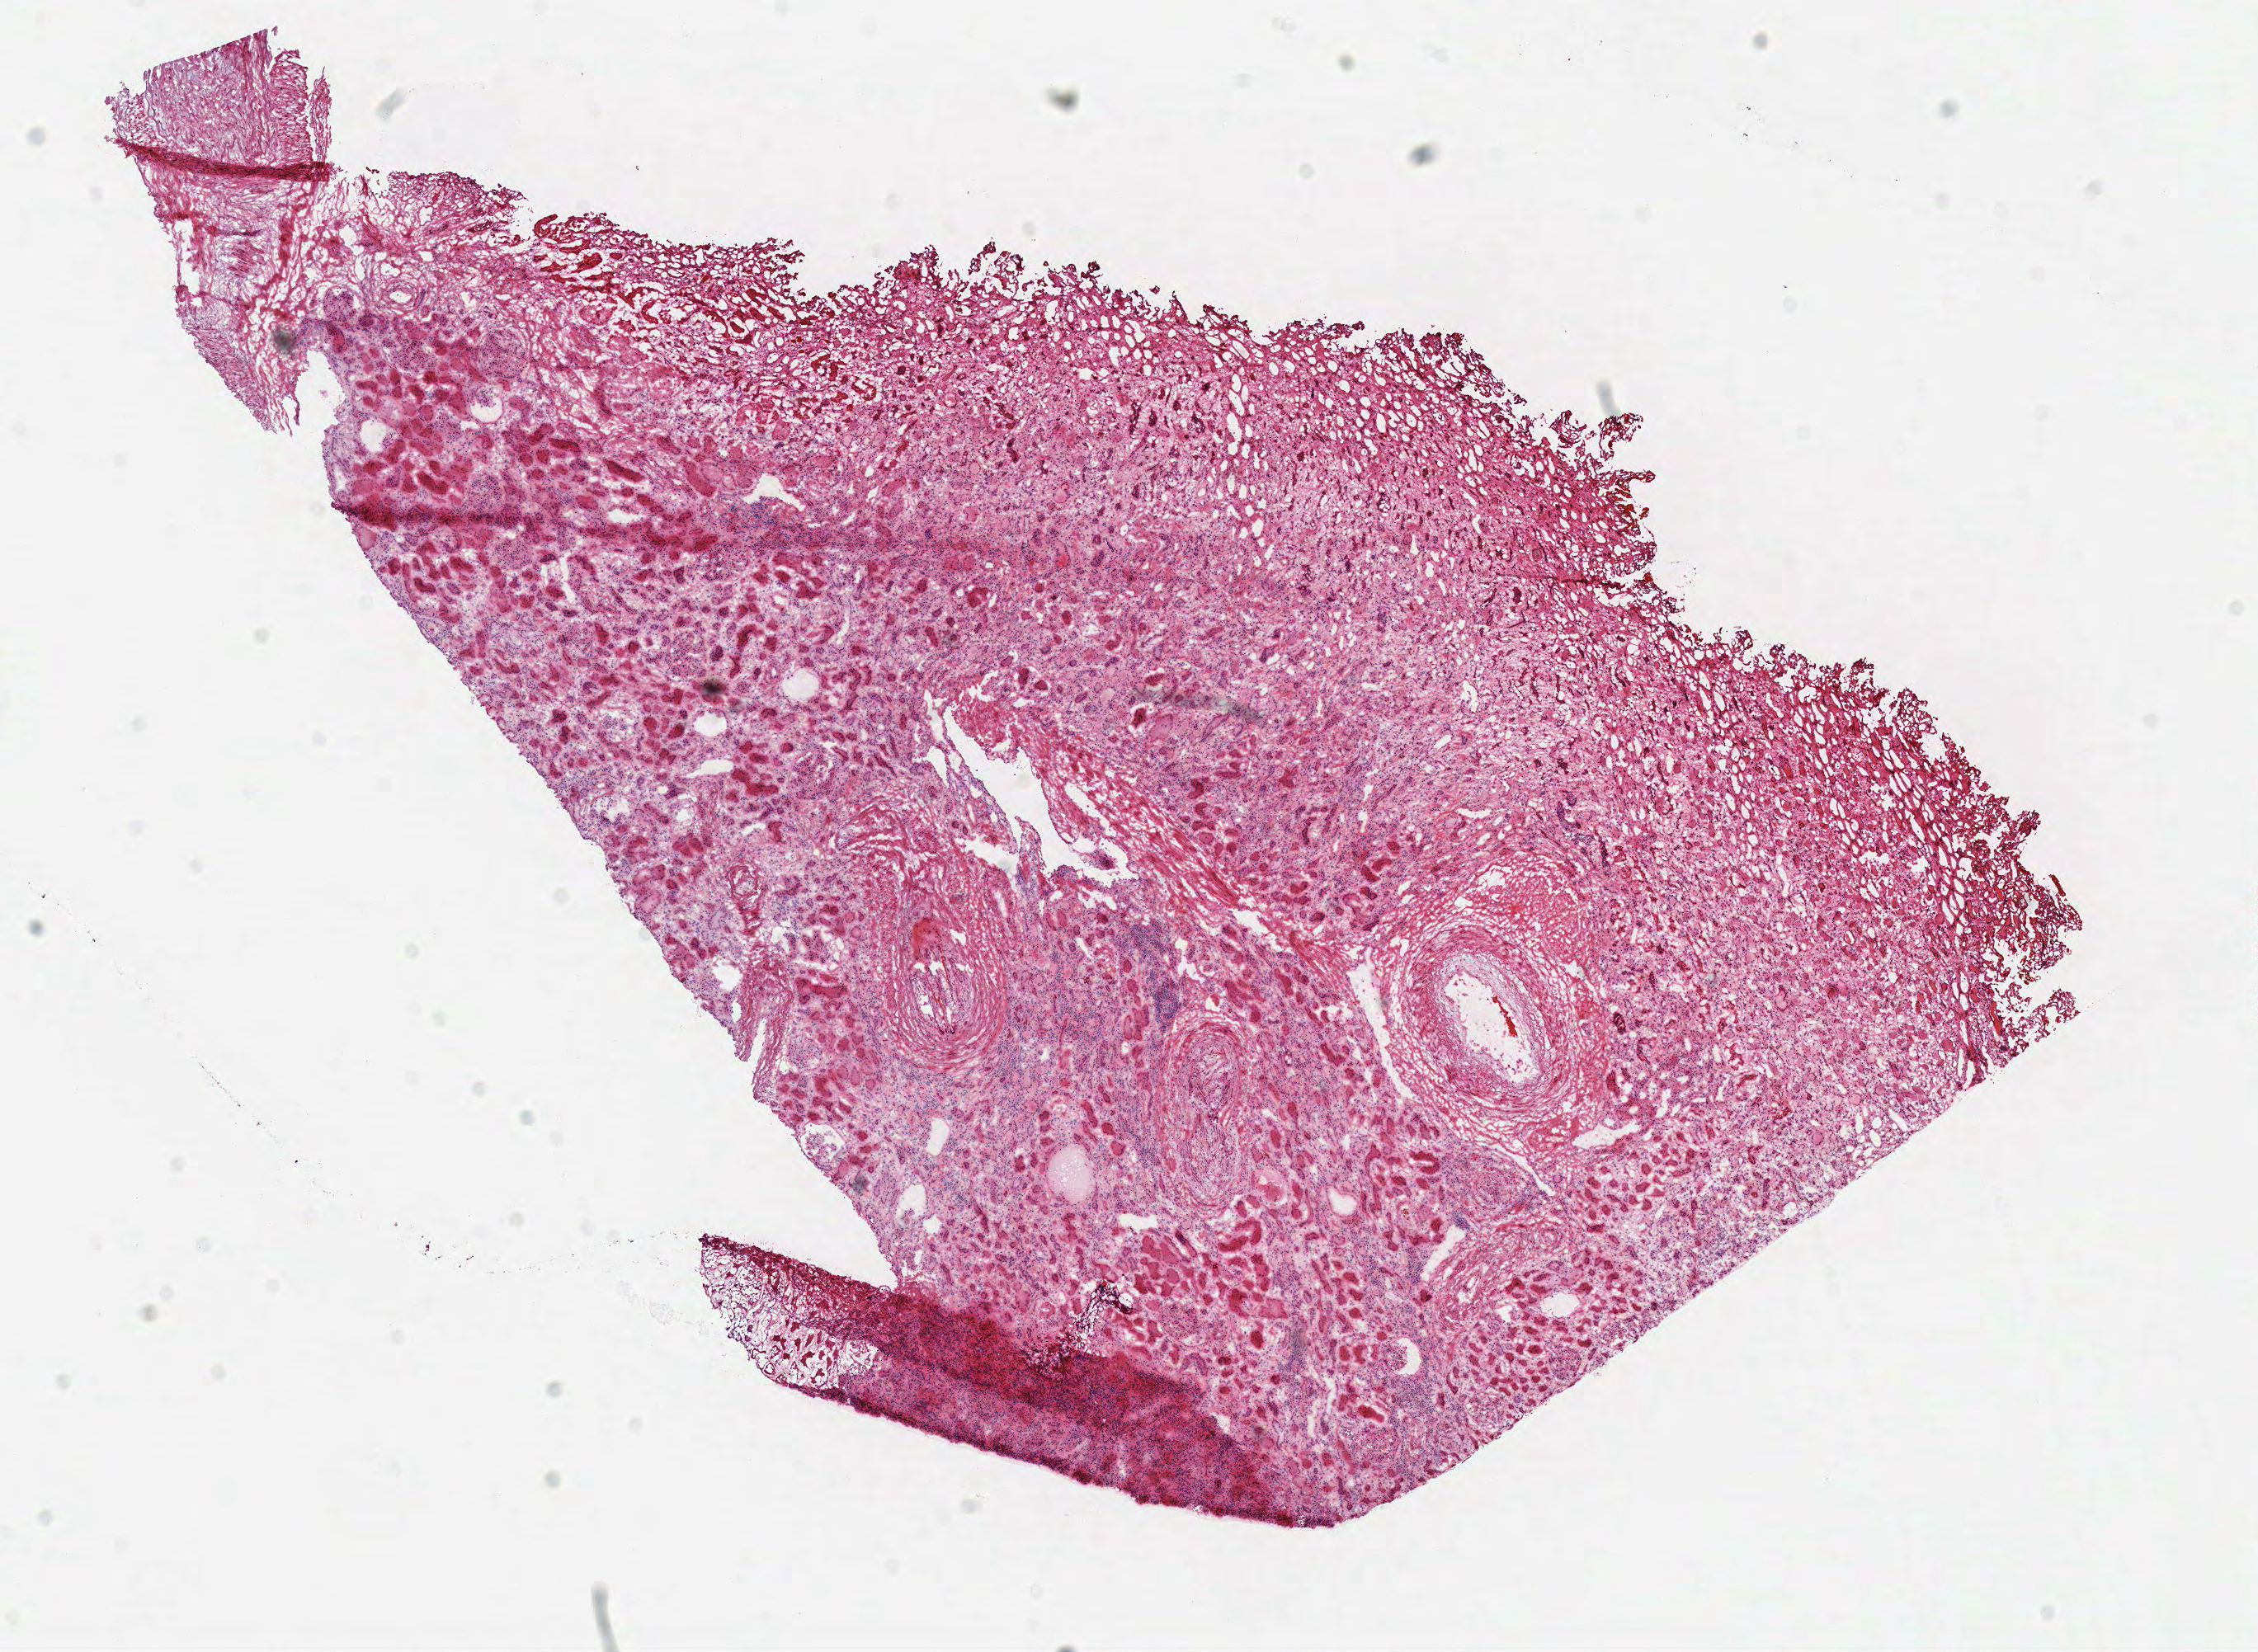
Digitized H&E-stained tissue section (whole slide) — shown as a low-resolution overview of the whole scanned area (about 10.8 x 7.9 mm), frozen section from the top of the tissue portion, solid tissue normal (non-tumour tissue) sample from the kidney. Male patient; age at initial diagnosis 69 years.
• this section: solid tissue normal sample (biorepository sample class)
• patient diagnosis: Papillary adenocarcinoma, NOS